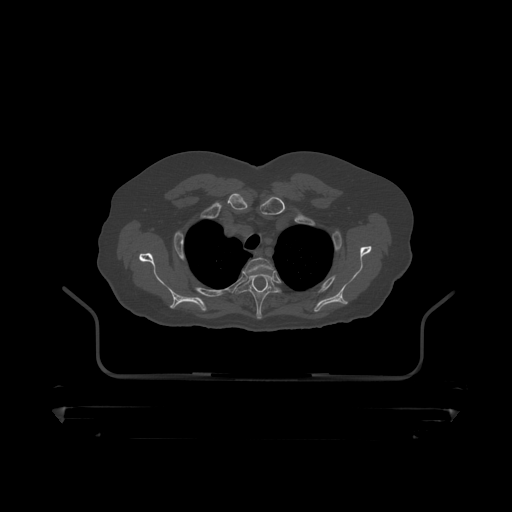
CT including the spine, one axial slice. Position 361 of 390 along the scan axis. 120 kVp. Bone window (W 1800 / L 400 HU). 1.25 mm slice thickness. 512 × 512 image matrix, field of view 650 × 650 mm. Patient: male, 60 years. Case-level facts recorded for this patient, not image findings: primary cancer: prostate.
Annotated regions visible in this slice (semi-automatically segmented with operator editing):
- T2 vertebra: bounding box (x1, y1, x2, y2) in pixels: (245, 258, 274, 273)
- T3 vertebra: (236, 271, 283, 319)